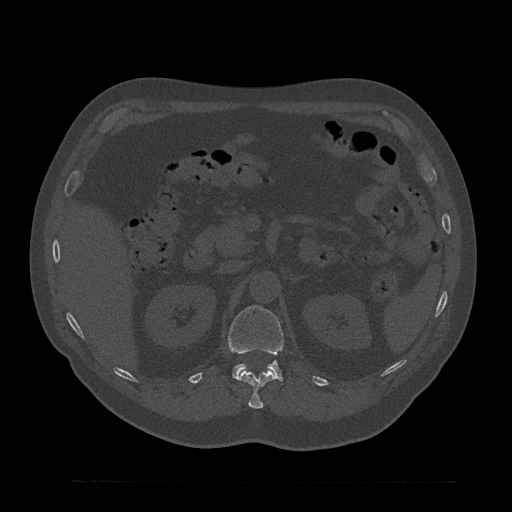
CT including the spine, one axial slice. Position 194 of 797 along the scan axis. 120 kVp. Bone window (W 1800 / L 400 HU). 0.5 mm slice thickness. 512 × 512 image matrix, field of view 430 × 430 mm. Male patient, age 61 years. Case-level facts recorded for this patient, not image findings: primary cancer: prostate.
Structures marked on this image (semi-automatically segmented with operator editing):
- L1 vertebra: bounding box (x1, y1, x2, y2) in pixels: (228, 306, 284, 382)
- T12 vertebra: (237, 369, 276, 409)